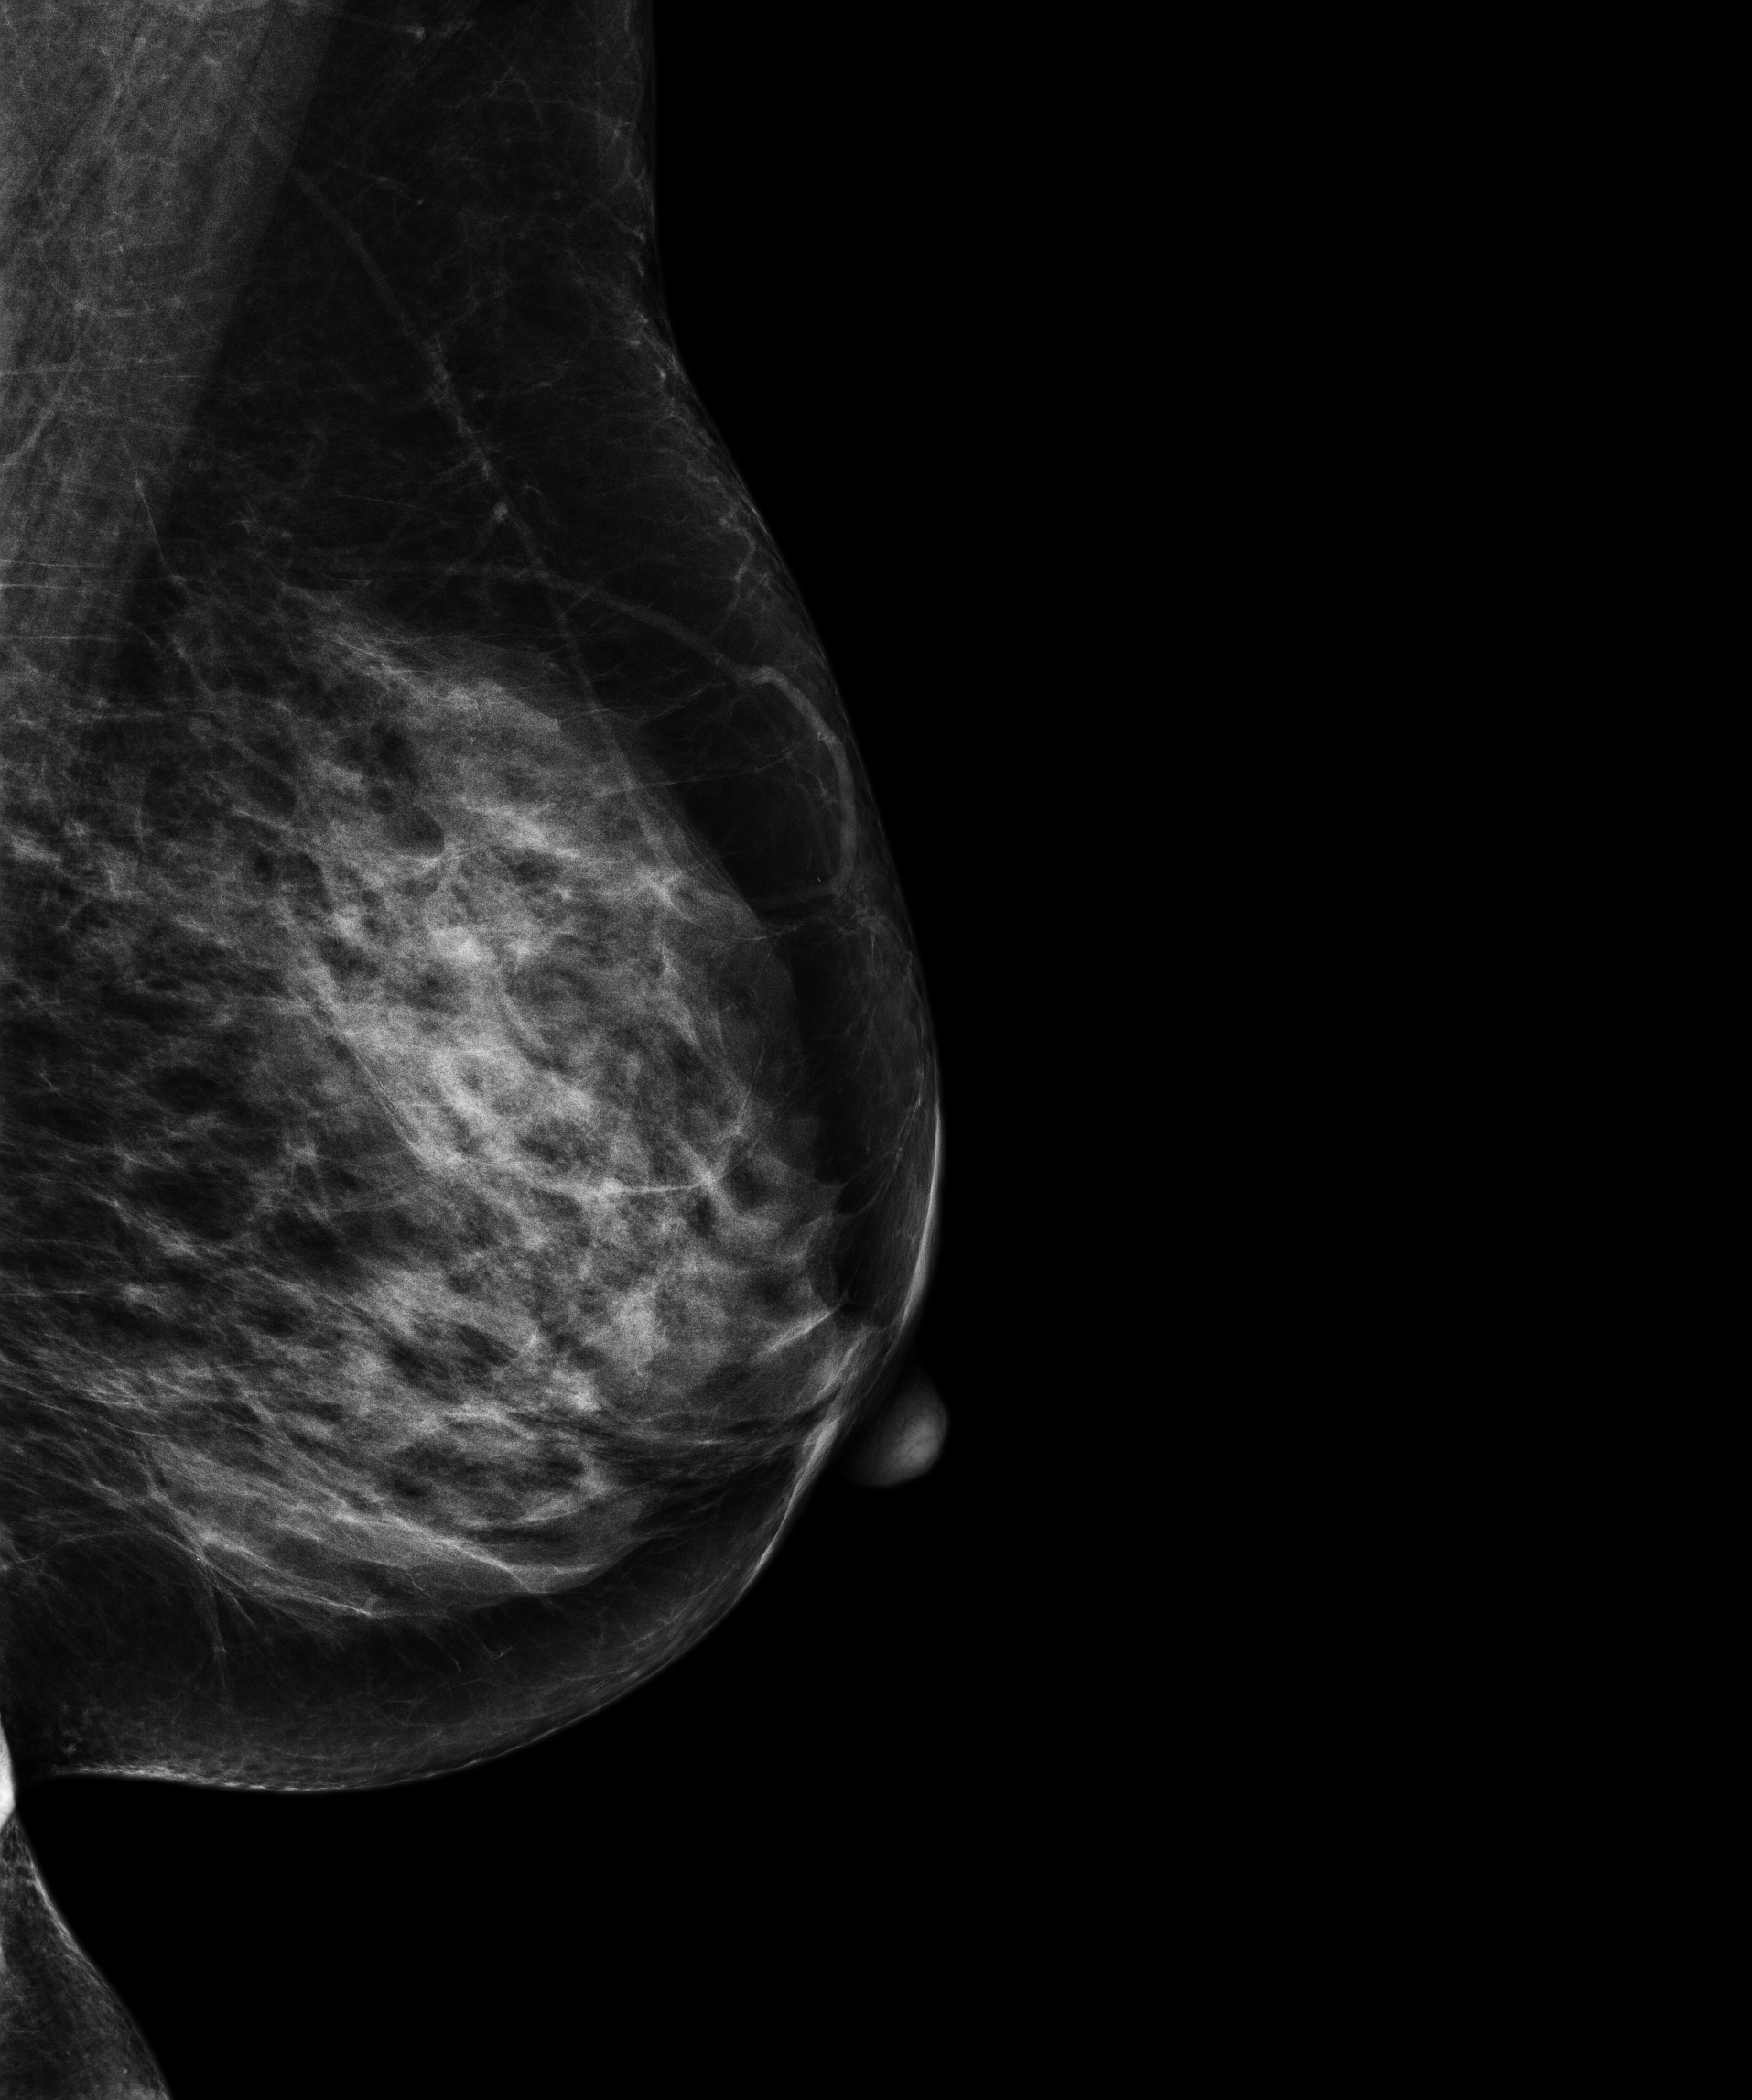
Annual screening mammography examination; compressed breast thickness 54 mm. Female patient, age 68 years.
Image type: full-field digital mammogram. Breast: left. Projection: medio-lateral oblique projection.